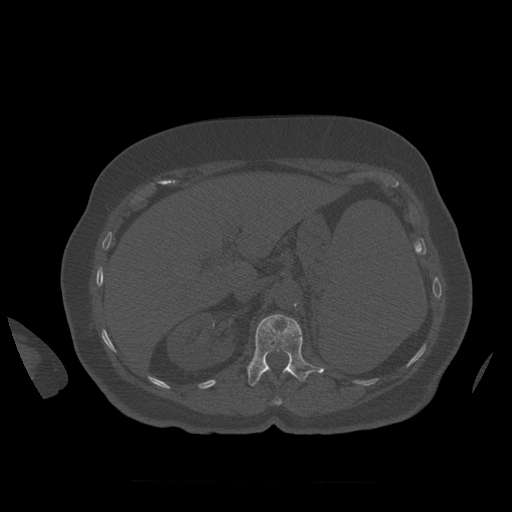
CT including the spine, one axial slice; position 283 of 399 along the scan axis; reconstruction kernel STANDARD; 120 kVp; bone window (W 1800 / L 400 HU); 1.25 mm slice thickness; 512 × 512 image matrix. Patient age 81 years. Case-level facts recorded for this patient, not image findings: primary cancer: renal; vertebrae with lytic lesions (as recorded): L1.
Structures marked on this image (semi-automatically segmented with operator editing):
- L1 vertebra: bounding box (x1, y1, x2, y2) in pixels: (247, 314, 325, 386)
- T12 vertebra: (273, 399, 282, 405)